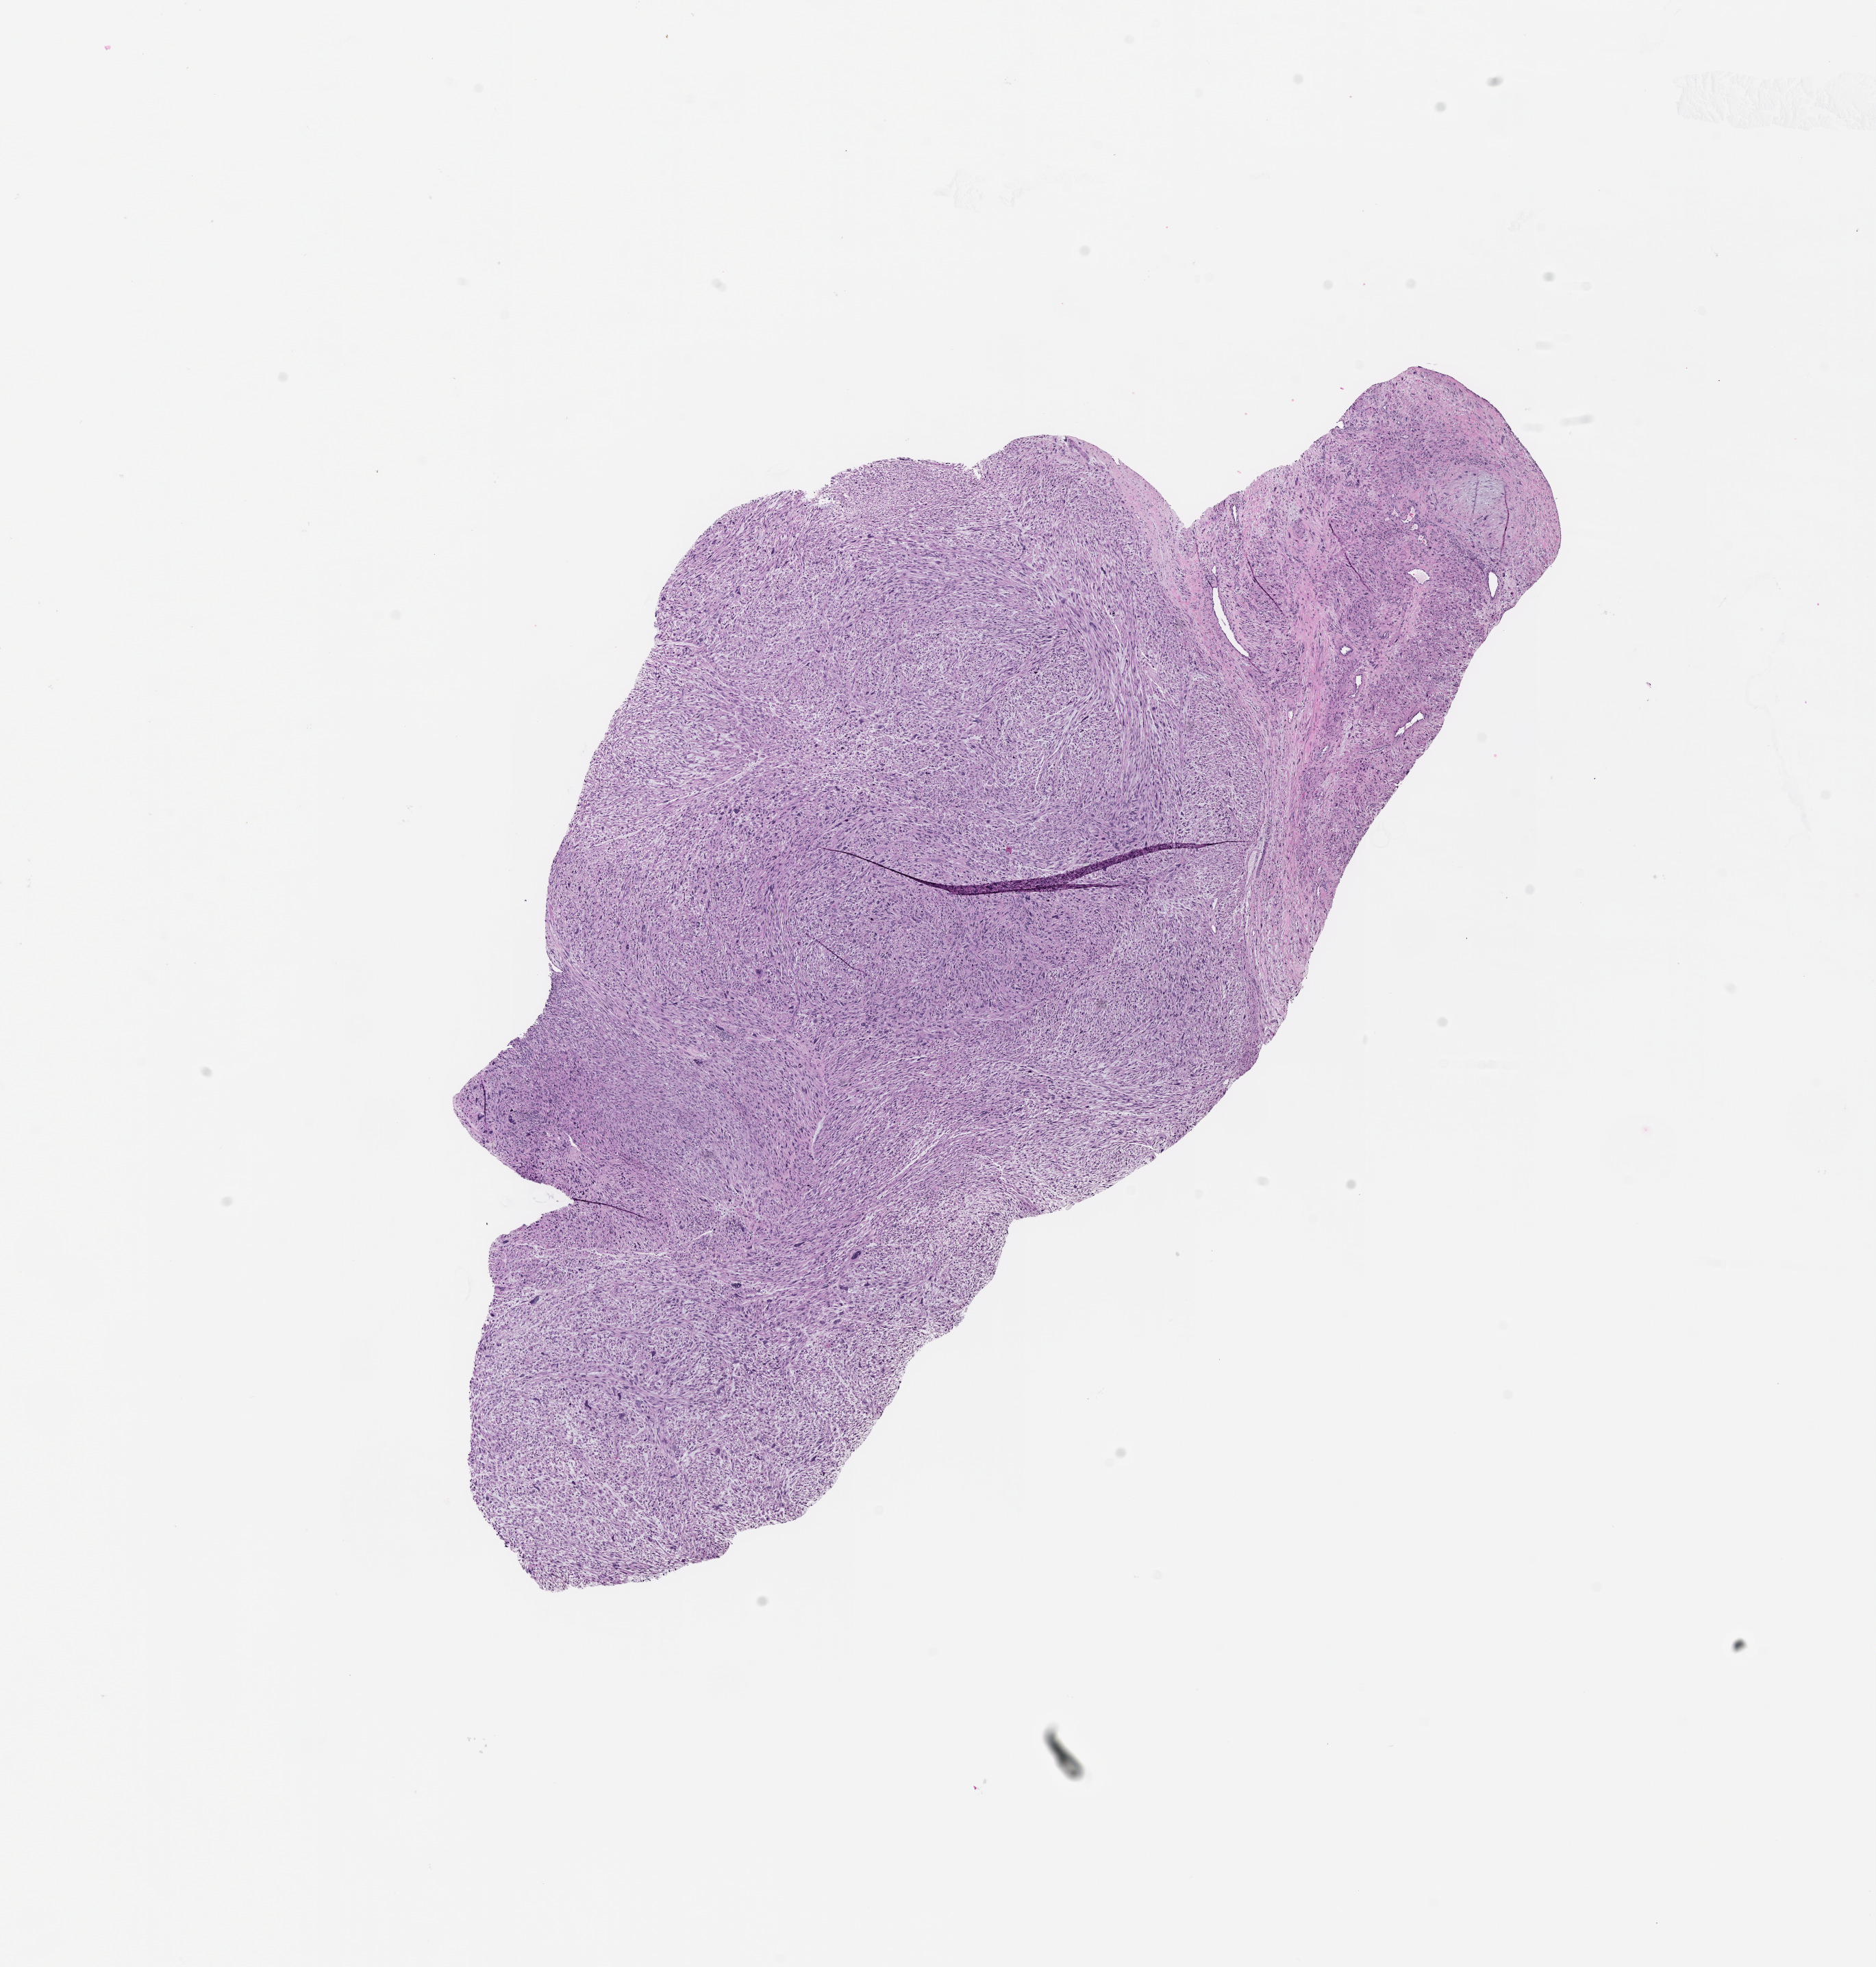
Digitized H&E-stained tissue section (whole slide) — shown as a low-resolution overview of the whole scanned area (about 11.0 x 11.6 mm).
Patient diagnosis (cohort enrolment): sarcoma (site not recorded at cohort level).